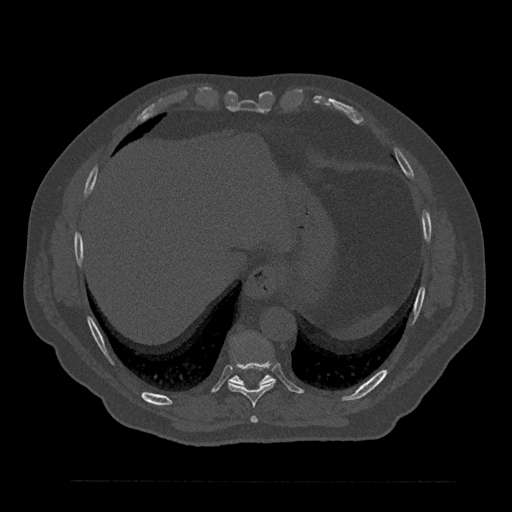
CT including the spine, one axial slice. Slice 387 of 797 in the series (ordered by position). Reconstruction kernel Br40s/3. Bone window (W 1800 / L 400 HU). 512 × 512 image matrix, field of view 430 × 430 mm. Male patient, age 61 years. Case-level facts recorded for this patient, not image findings: primary cancer: prostate.
Outlined on this slice (semi-automatically segmented with operator editing):
- T10 vertebra: bounding box [x1, y1, x2, y2] px = [228, 333, 274, 386]
- T8 vertebra: [250, 416, 258, 423]
- T9 vertebra: [228, 362, 275, 407]